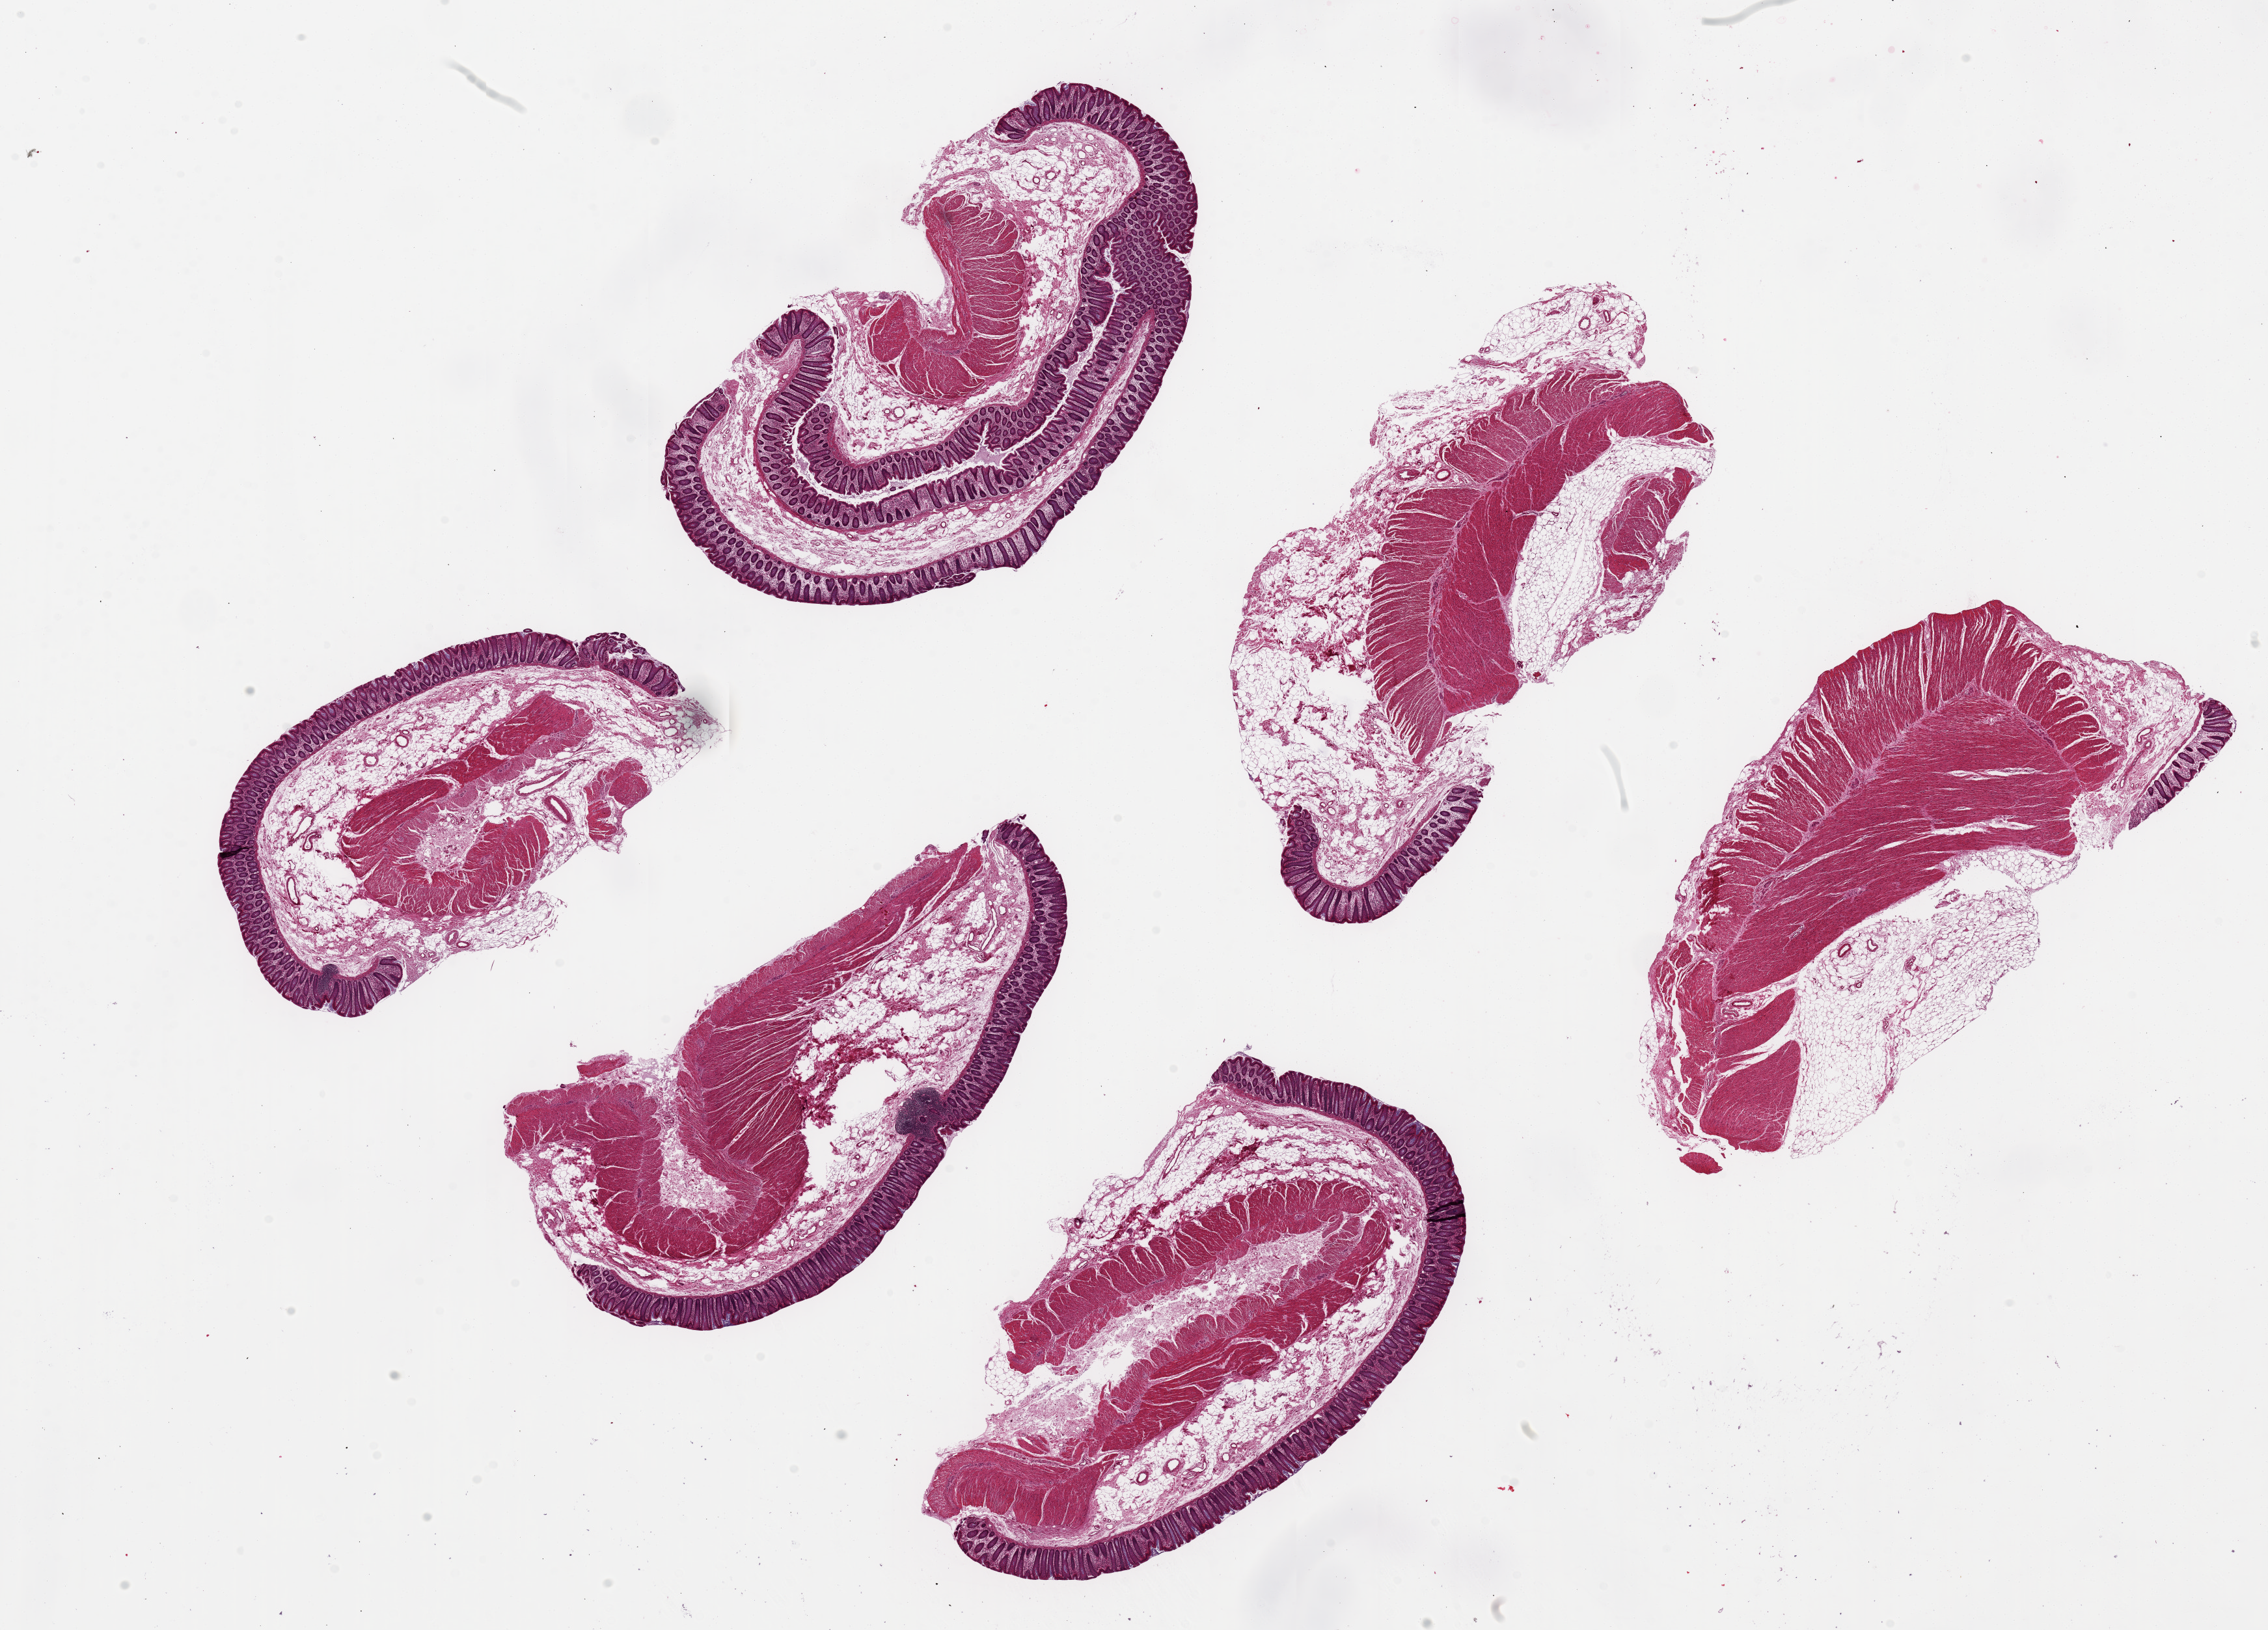
Whole-slide image, hematoxylin and eosin (H&E) stain, brightfield — low-resolution overview of the scanned area, about 27.6 x 19.8 mm (slide scanned at 20x), PAXgene-fixed paraffin-embedded (PFPE) section, target tissue: transverse colon, donor tissue sample. Male donor.
Review note (as recorded): 6 pieces up to 7.5x4 mm; good mucosa.